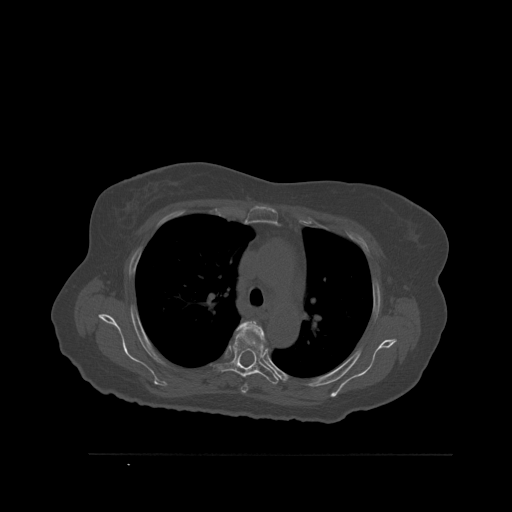
CT including the spine, one axial slice. Position 398 of 527 along the scan axis. Bone window (W 1800 / L 400 HU). 512 × 512 image matrix, field of view 470 × 470 mm. Patient: female, 73 years. From the clinical record (not read from this slice): primary cancer: breast; vertebrae with lytic lesions (as recorded): L2.
Annotated regions visible in this slice (semi-automatically segmented with operator editing):
- T4 vertebra: bounding box [x1, y1, x2, y2] px = [236, 320, 266, 393]
- T5 vertebra: [214, 330, 279, 385]